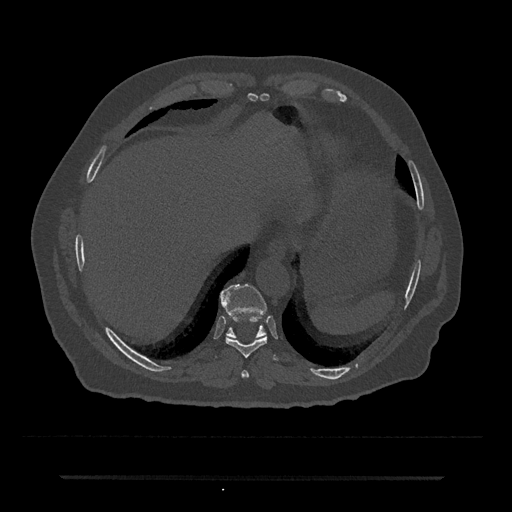
CT including the spine, one axial slice; position 263 of 797 along the scan axis; 120 kVp; bone window (W 1800 / L 400 HU); 0.5 mm slice thickness; 512 × 512 image matrix, field of view 437 × 437 mm. Patient: male, 69 years. From the clinical record (not read from this slice): primary cancer: prostate.
Outlined on this slice (semi-automatically segmented with operator editing):
- T10 vertebra: bounding box [x1, y1, x2, y2] px = [220, 284, 267, 339]
- T8 vertebra: [241, 370, 249, 378]
- T9 vertebra: [225, 336, 278, 360]